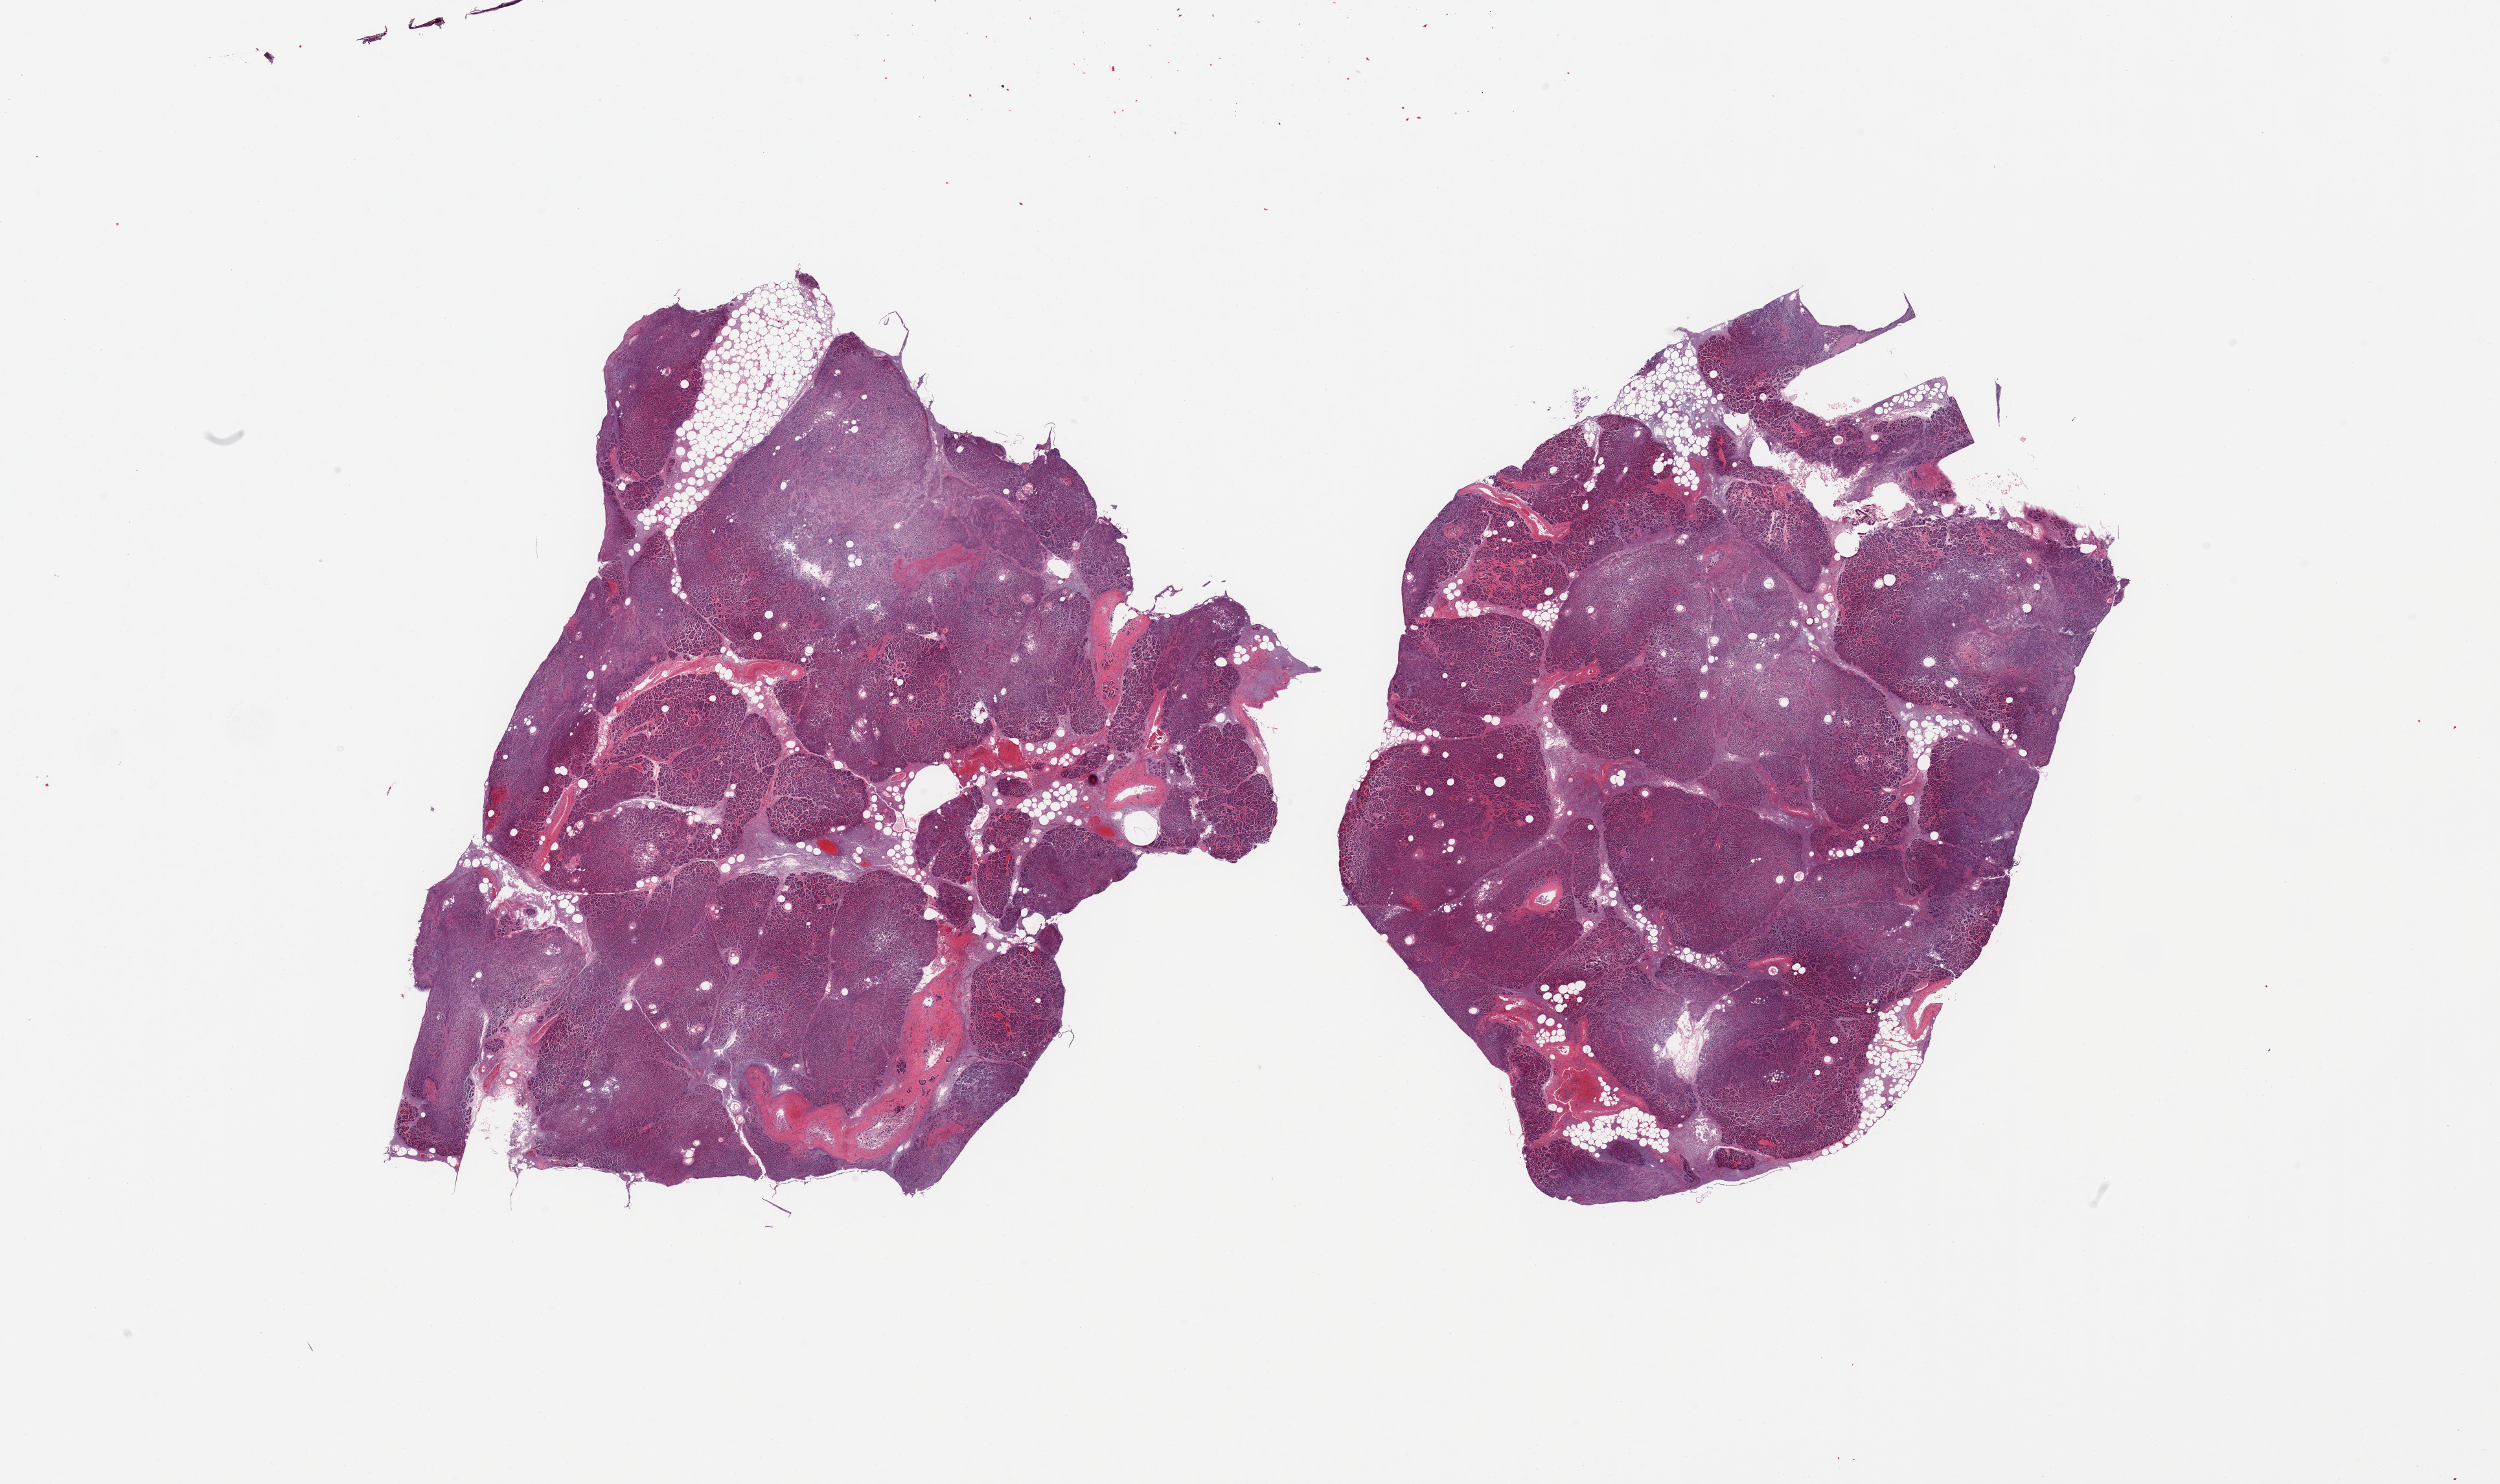
Digitized haematoxylin and eosin-stained section, whole scanned area (about 30.5 x 18.1 mm, slide scanned at 20x) shown as a low-resolution overview, PAXgene-fixed, paraffin-embedded tissue, sampled site (target tissue): pancreas, tissue donor sample.
* review note (as recorded): 2 pieces, saponification moderate-markedly advanced; Islets not visible